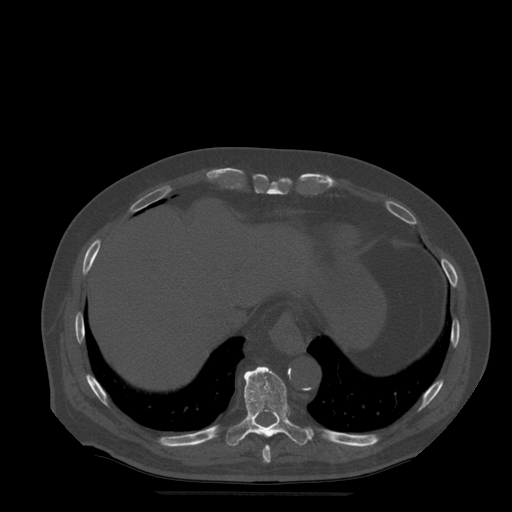
CT including the spine, one axial slice; slice 271 of 522 in the series (ordered by position); bone window (W 1800 / L 400 HU); 1.25 mm slice thickness; 512 × 512 image matrix, field of view 420 × 420 mm. Patient age 72 years. From the clinical record (not read from this slice): primary cancer: prostate.
Annotated regions visible in this slice (semi-automatically segmented with operator editing):
- T10 vertebra: bounding box [x1, y1, x2, y2] px = [226, 367, 313, 446]
- T9 vertebra: [263, 445, 271, 464]